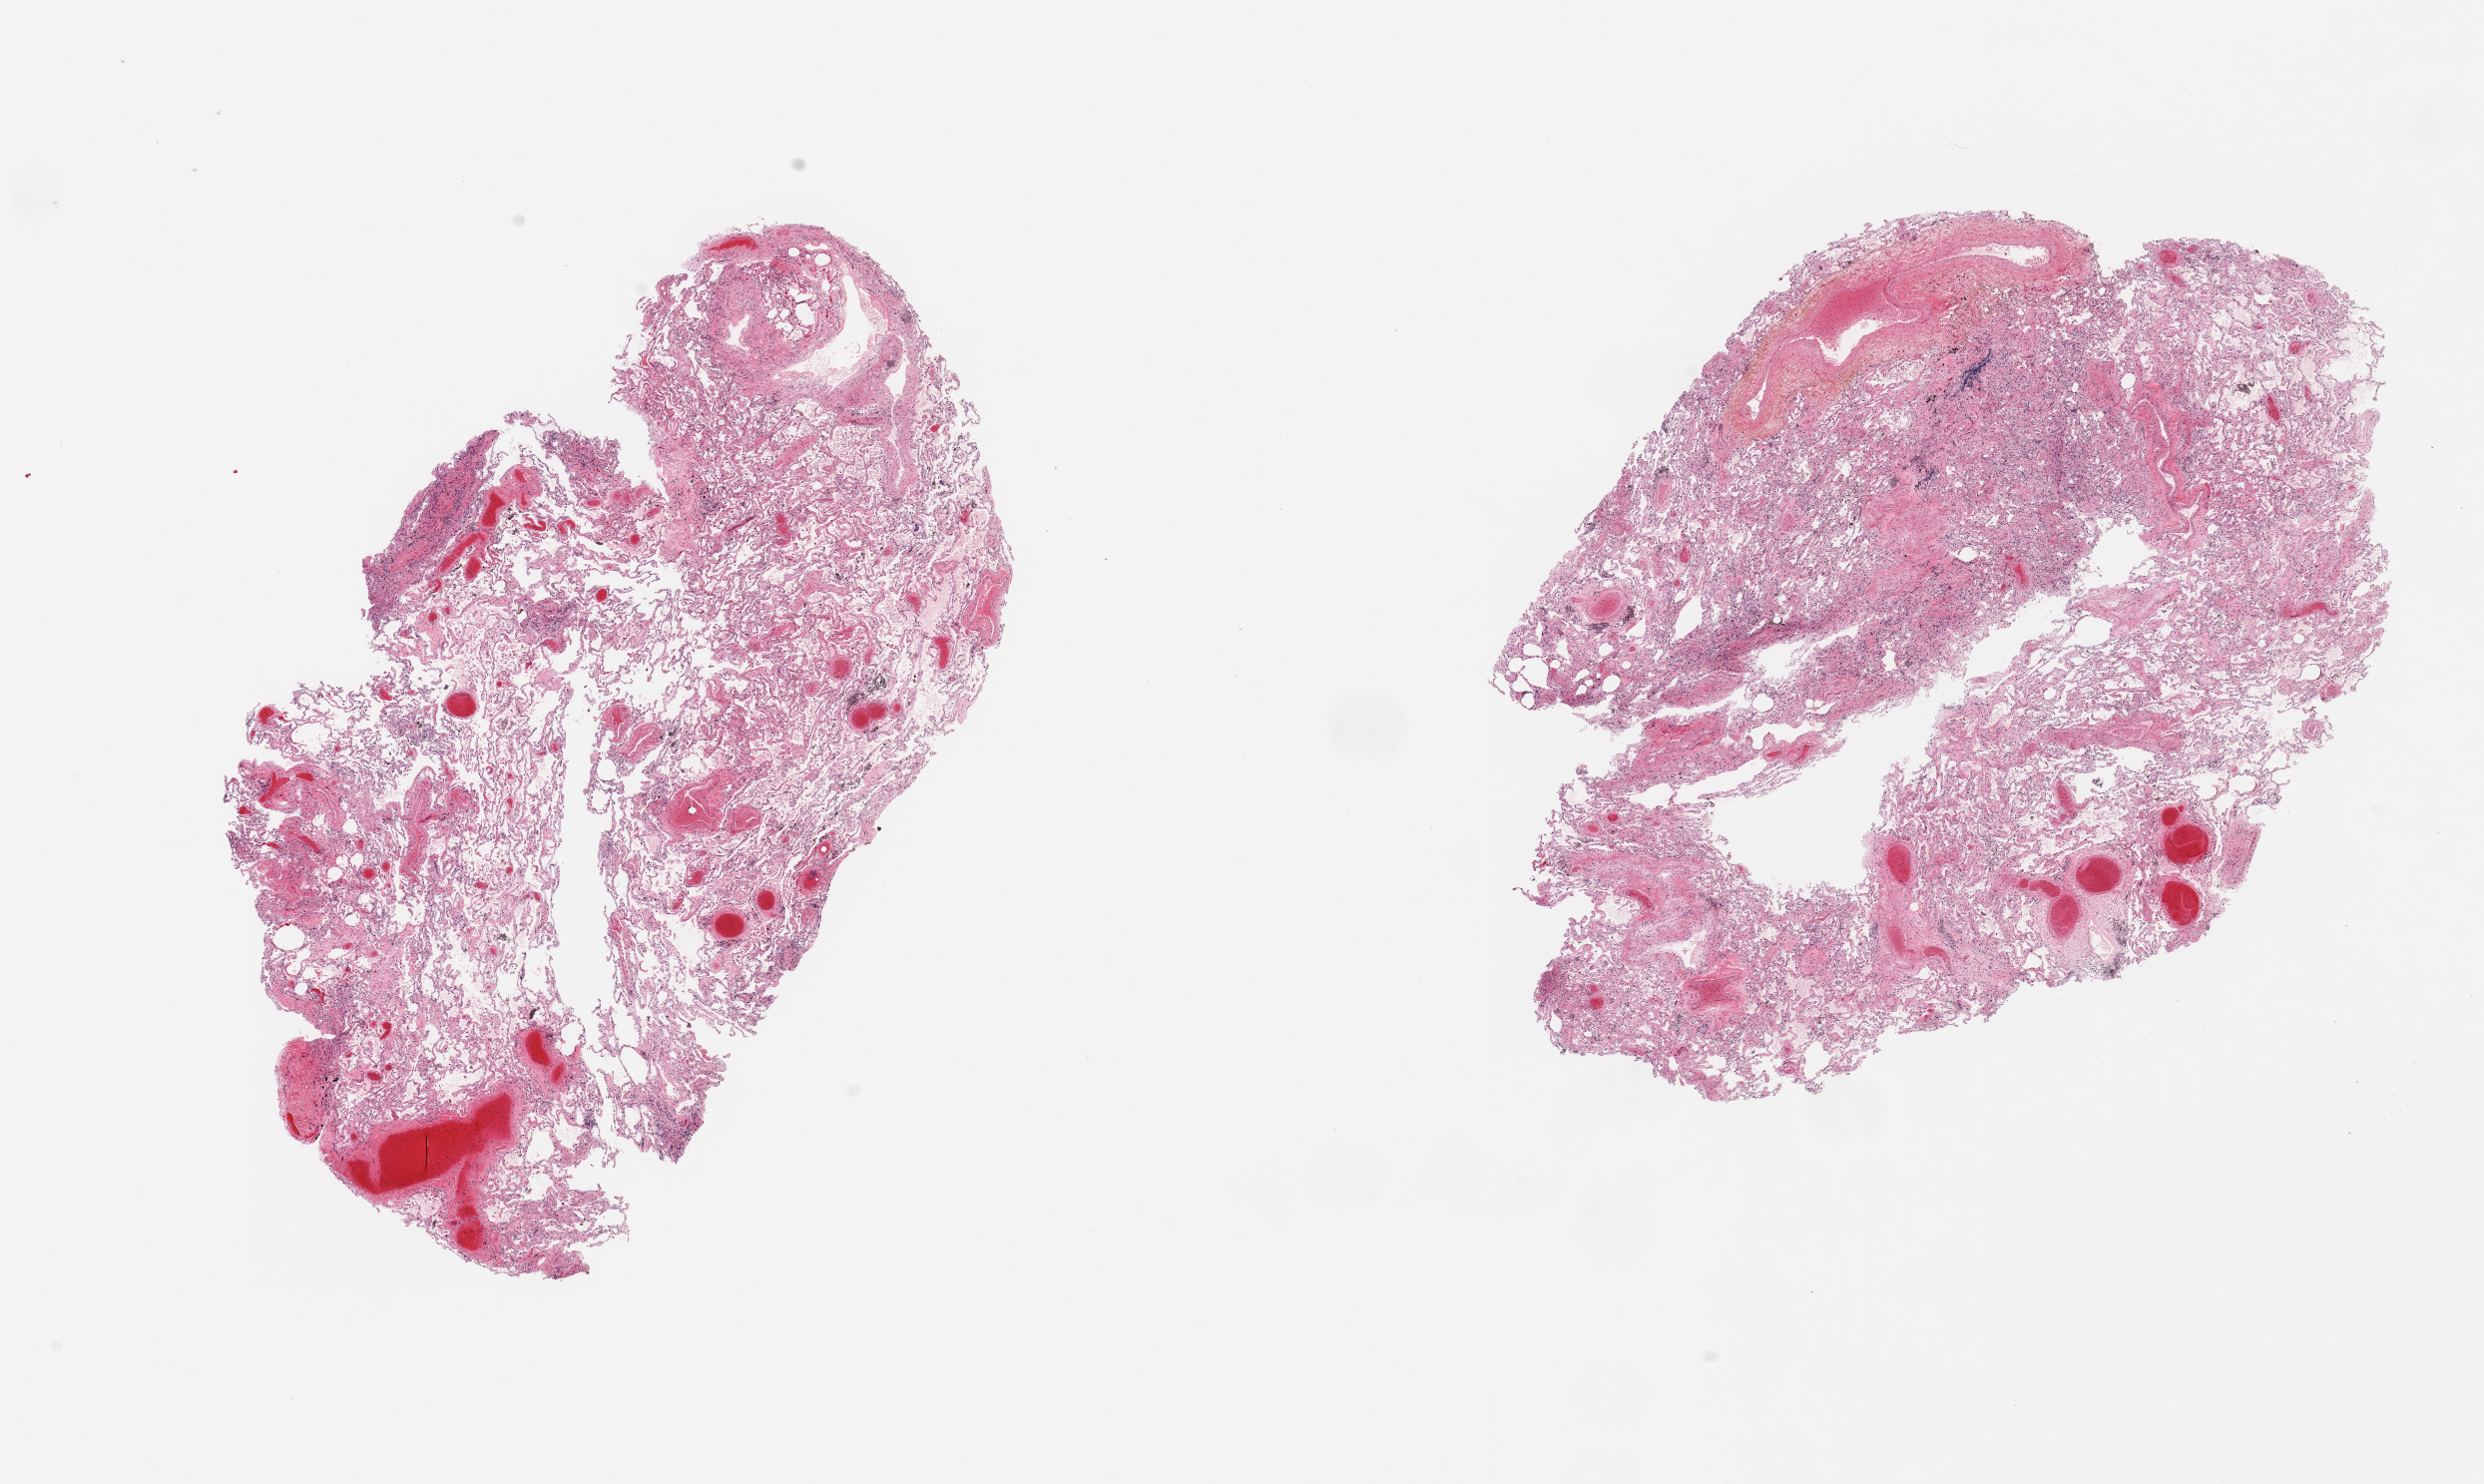
Whole-slide image, haematoxylin and eosin stain, shown as a low-resolution overview of the whole scanned area (about 19.7 x 11.8 mm, acquisition: 20x scan); PAXgene-fixed paraffin-embedded (PFPE) section; sampled site (target tissue): lung; donor tissue sample. Female donor.
Reviewer comment on this tissue sample: 2 pieces; pulmonary edema & congestion.